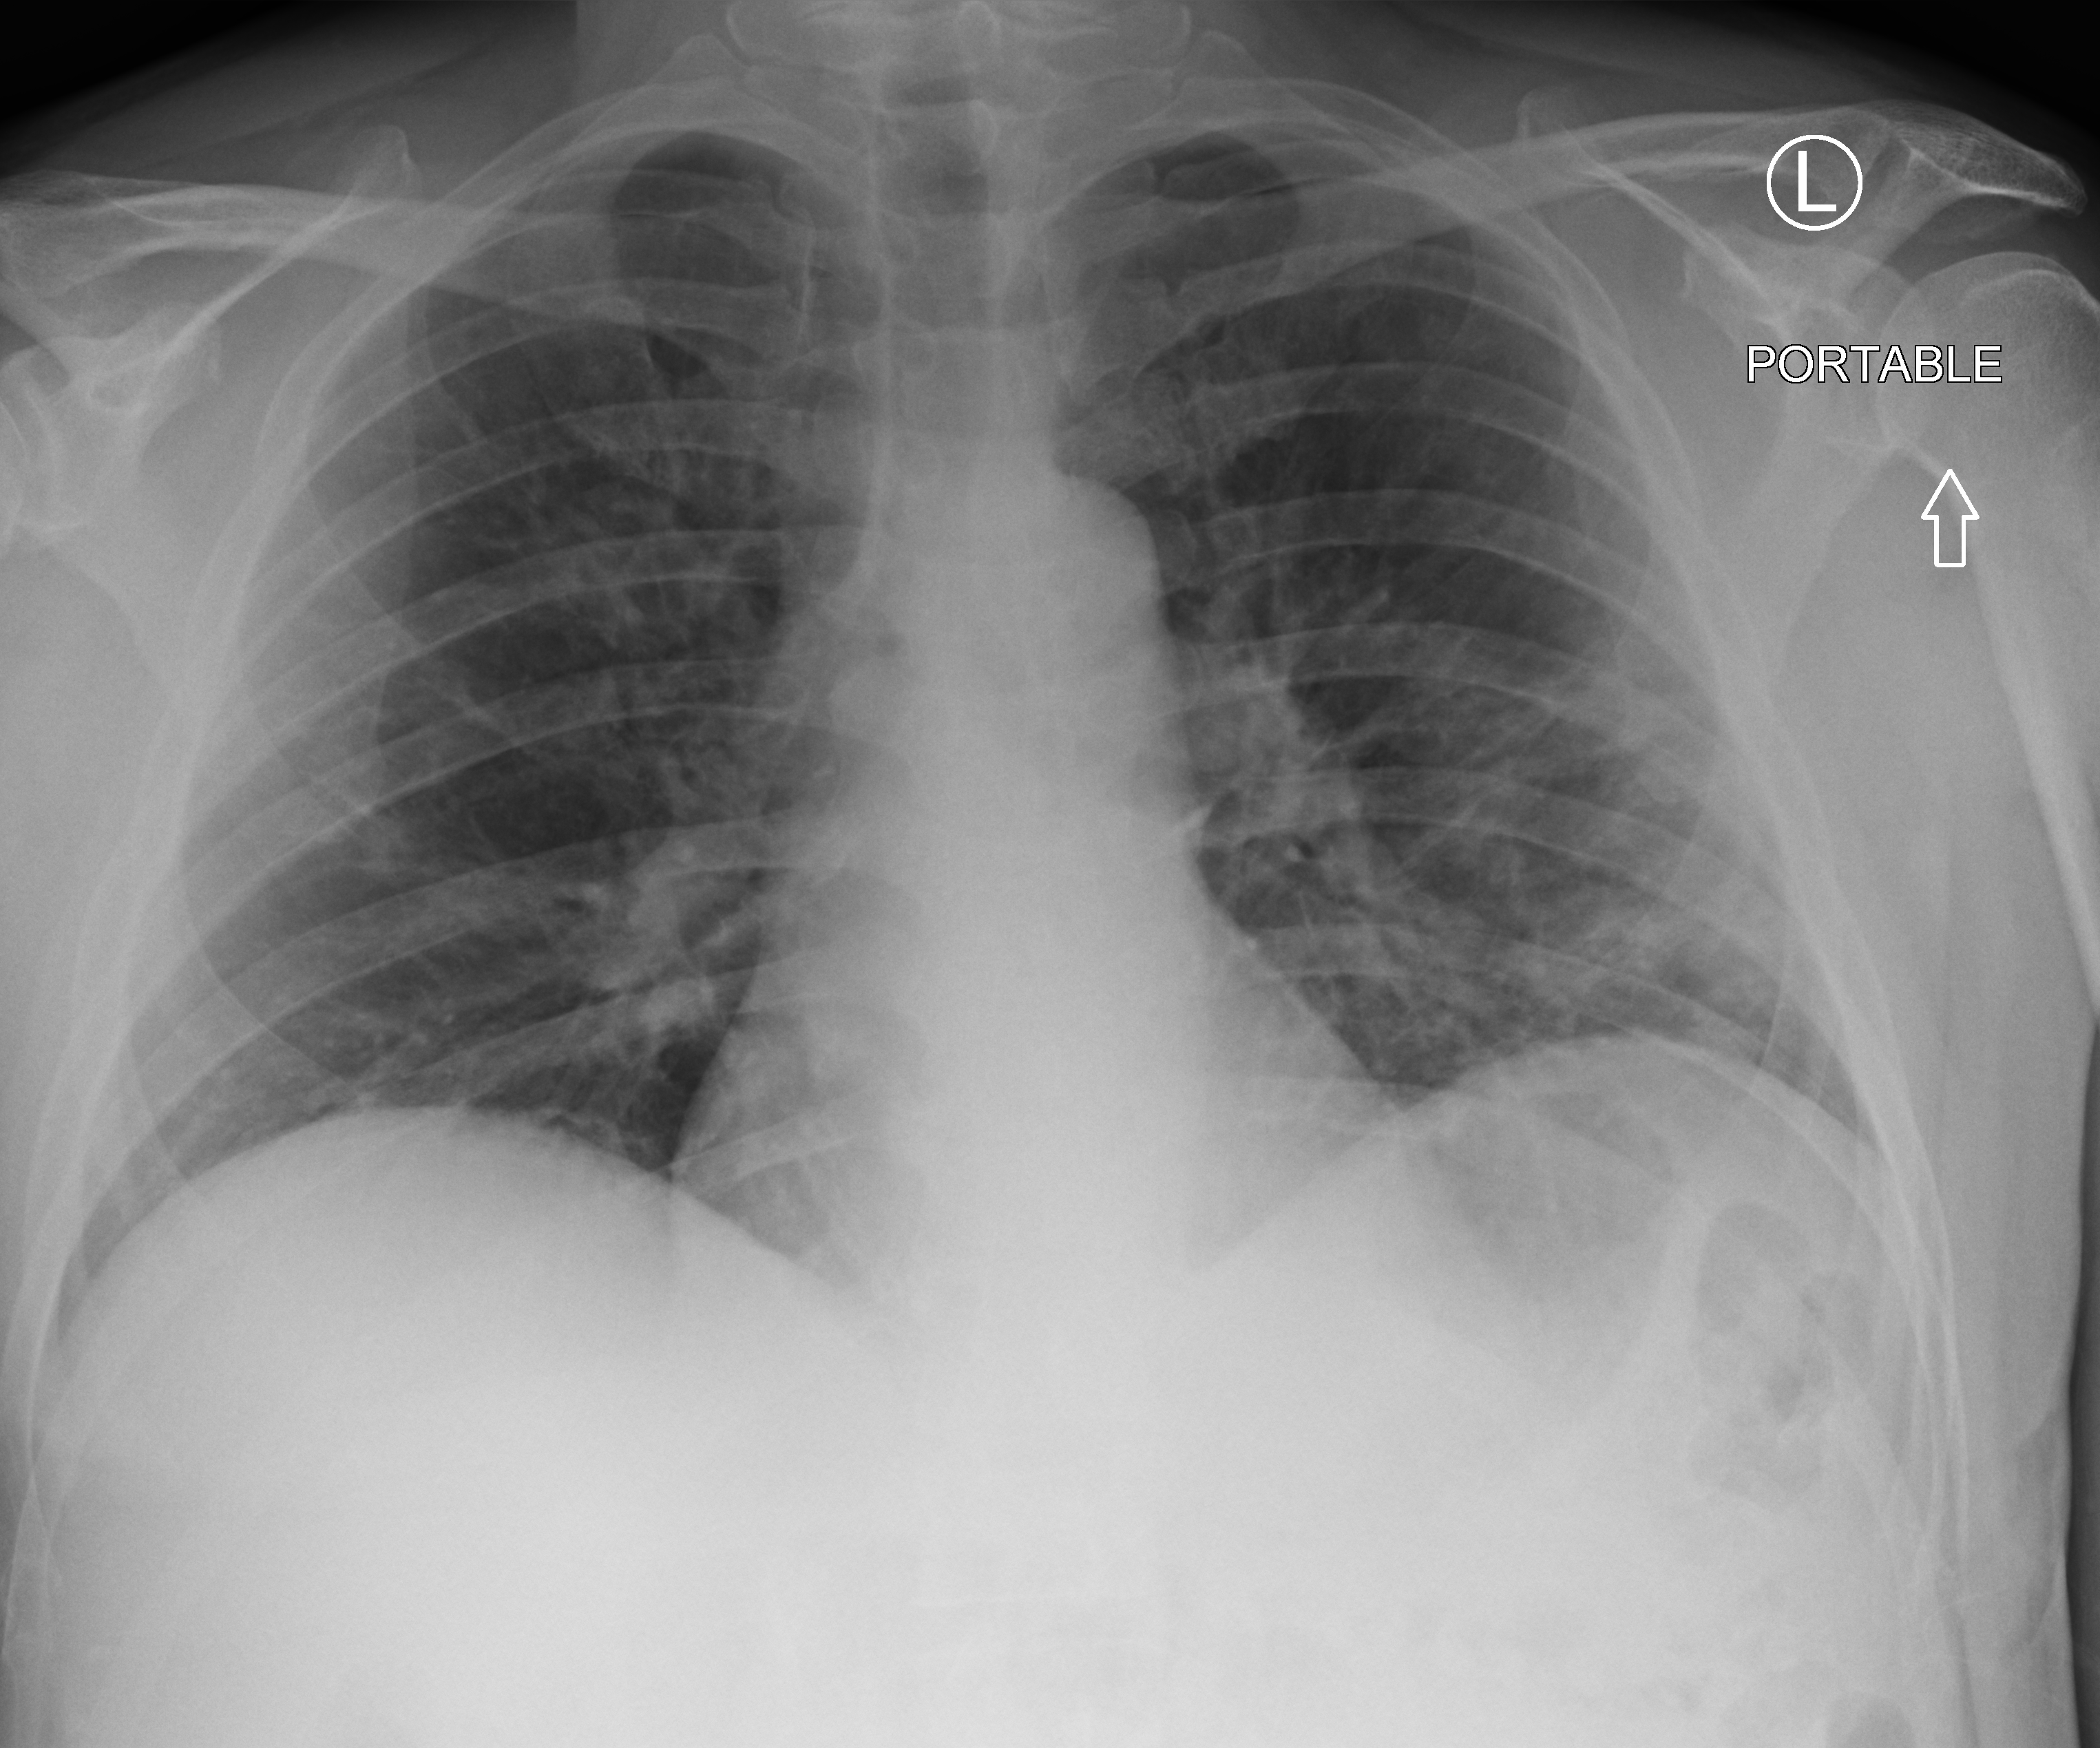
Bedside chest radiograph (computed radiography). Patient hospitalised with COVID-19; male, aged 18–59 years.
Hospital-stay facts (about this admission, not read from this image; timing relative to this image not recorded): admitted to intensive care during this hospital stay: no.